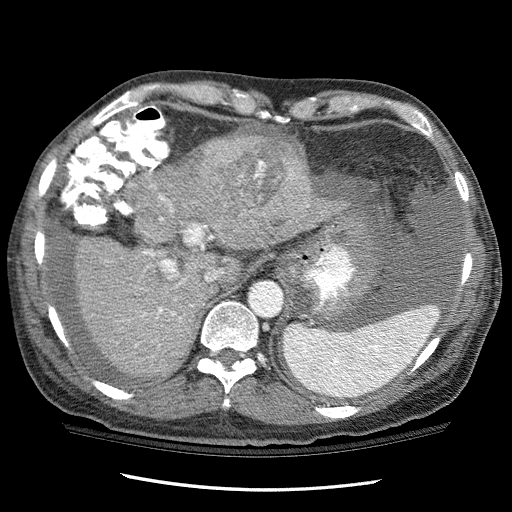
Contrast-enhanced abdominal CT (liver protocol), one axial slice; slice 82 of 114 in the series (ordered by position); 120 kVp; one of 3 acquisitions stored at this slice position; soft-tissue window (W 400 / L 40 HU); 2.5 mm slice thickness; 512 × 512 image matrix, field of view 360 × 360 mm. From the clinical record (not read from this slice): diagnosis: hepatocellular carcinoma (patient treated with transarterial chemoembolisation; whether this scan precedes or follows treatment is not stated here); TNM stage (as recorded): Stage-I; Child-Pugh class: C; tumour differentiation: well differentiated.
Annotated regions visible in this slice (semi-automatic segmentation, software-assisted and operator-edited):
- abdominal aorta: bounding box [x1, y1, x2, y2] px = [249, 283, 282, 317]
- liver parenchyma outside the tumour (the mass and vessels are separate outlines, so this box may not span the whole liver): [74, 144, 345, 376]
- mass: [196, 125, 315, 242]
- liver vessels: [142, 195, 213, 317]